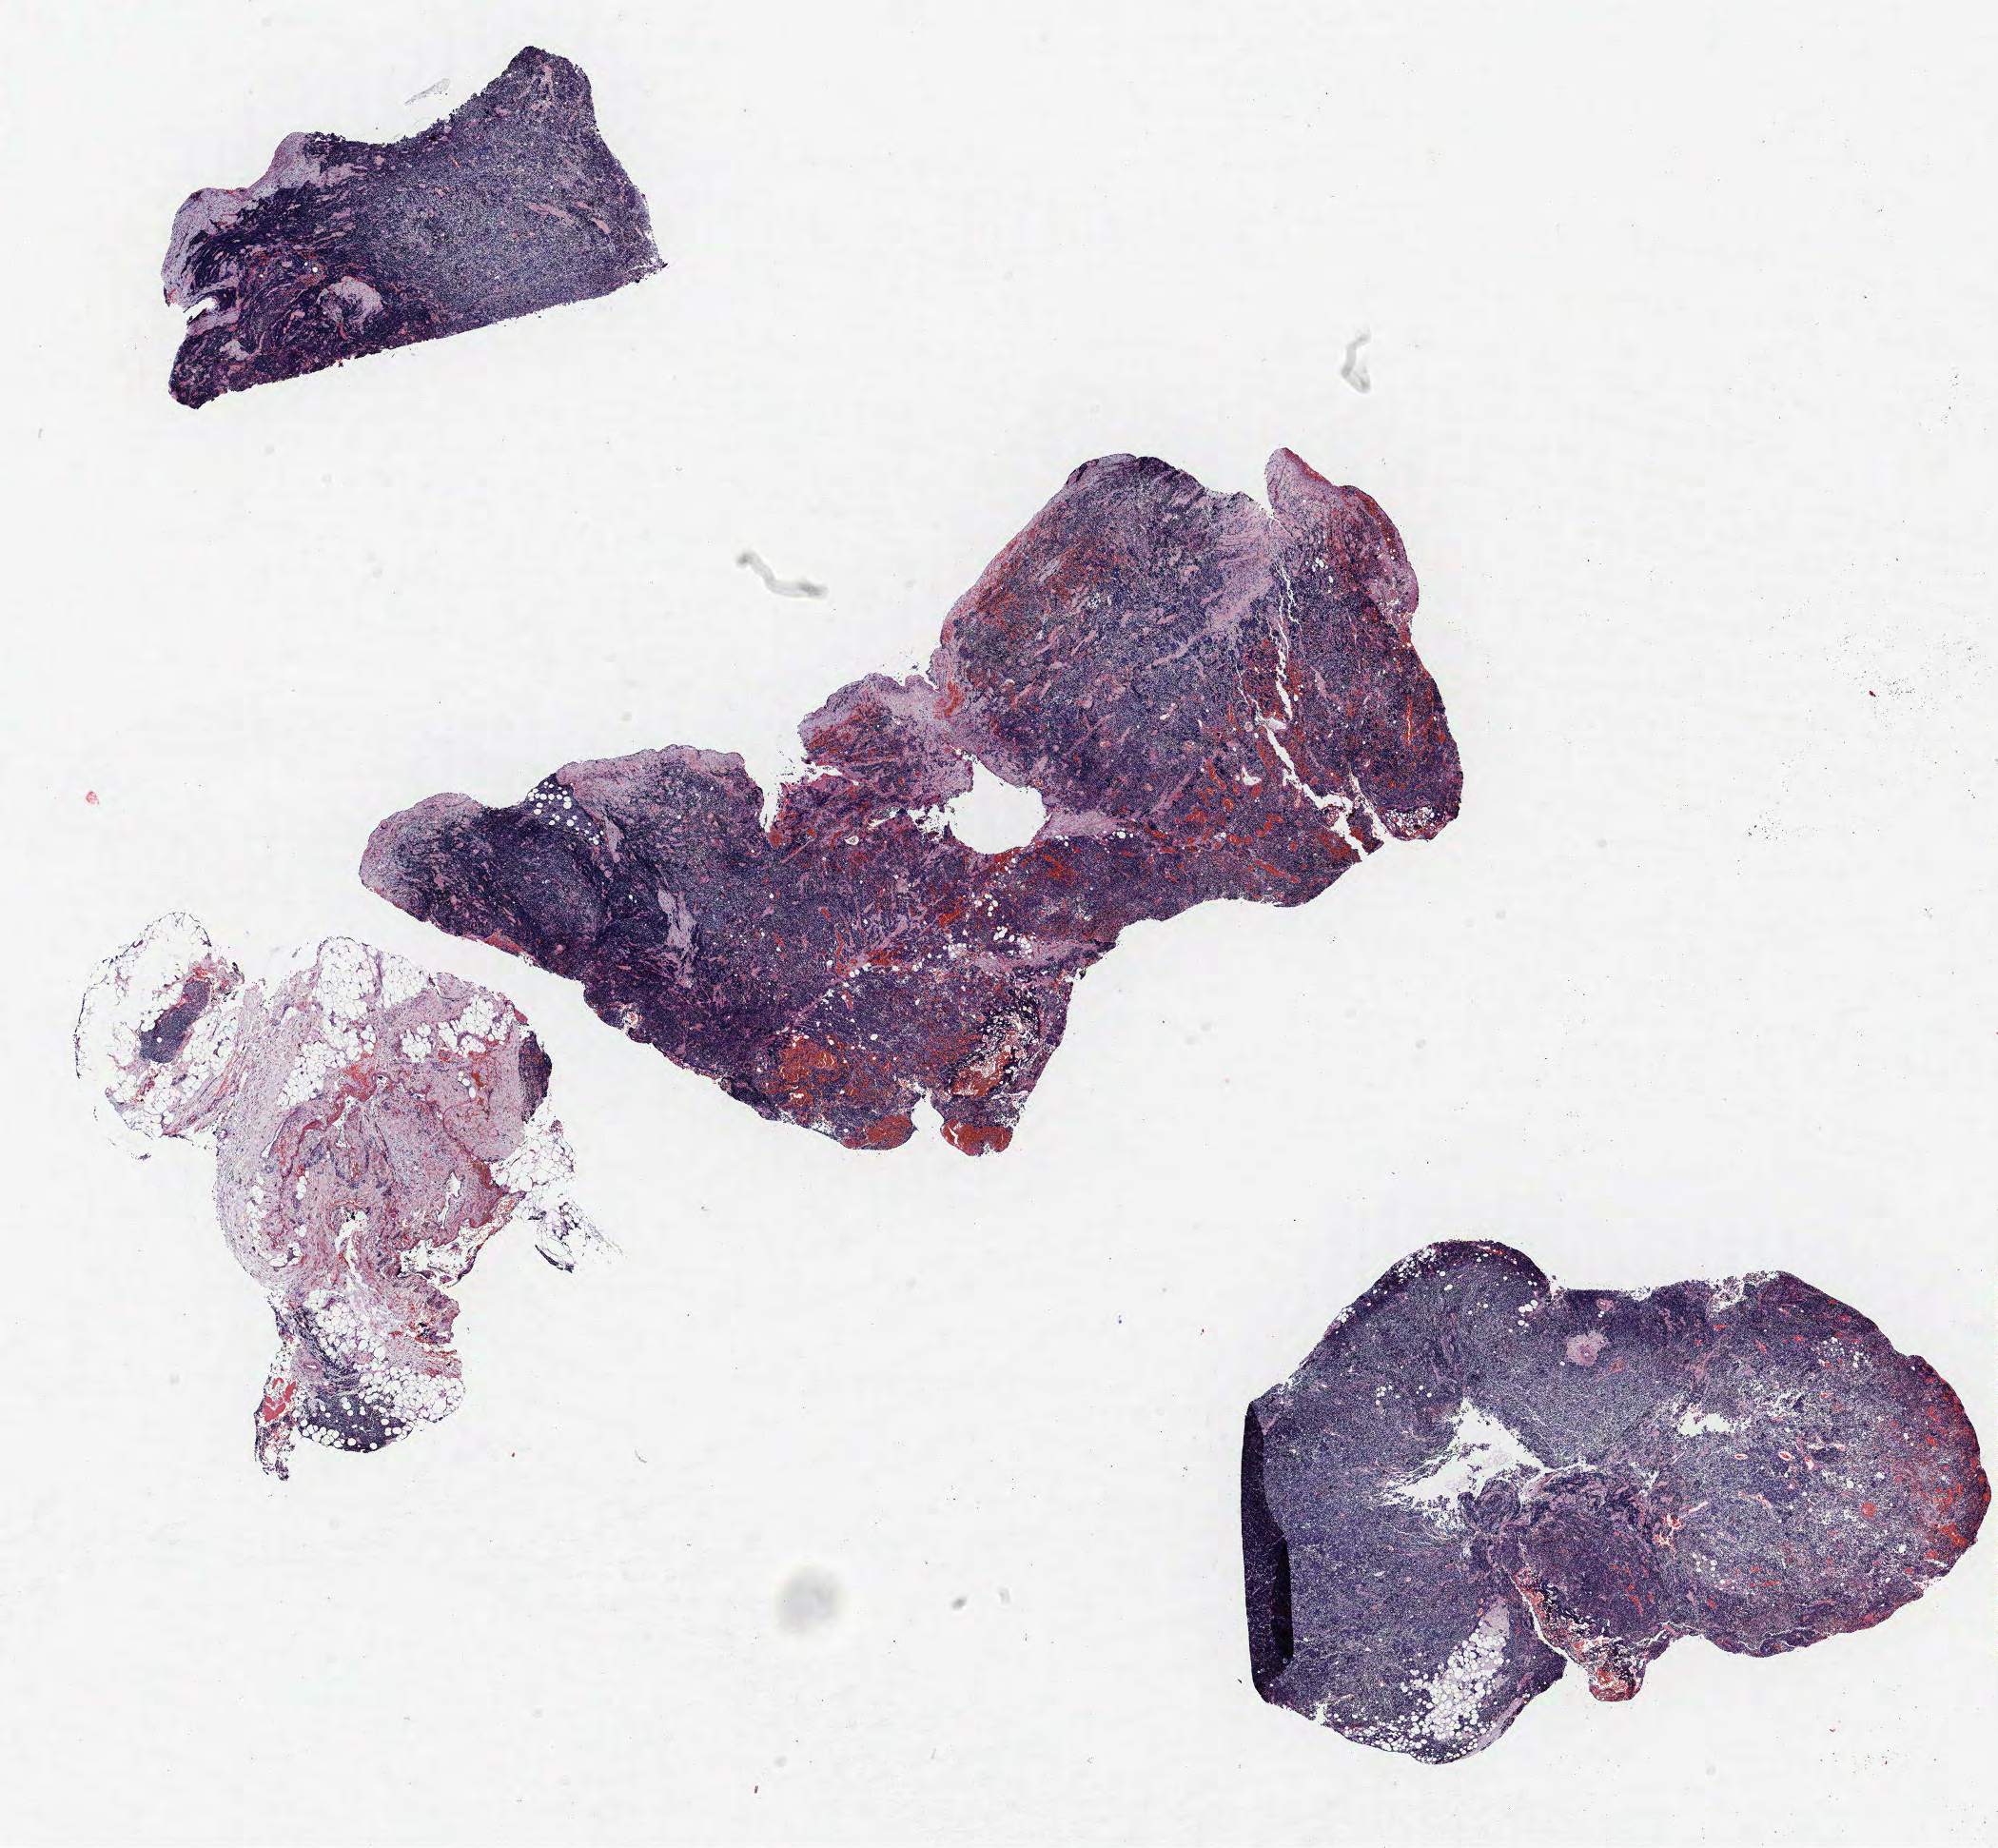
Whole-slide histology image, H&E-stained, low-resolution overview of the scanned area, about 16.8 x 15.5 mm; formalin-fixed paraffin-embedded (FFPE) section; lung tissue. Male patient, aged 68 at enrolment. Current smoker at enrolment.
Stage (AJCC 6th edition): IIIB. Tumour size (pathology): 20 mm. Primary tumour location (clinical record): right upper lobe. Participant's lung-cancer diagnosis: Small cell carcinoma, NOS.